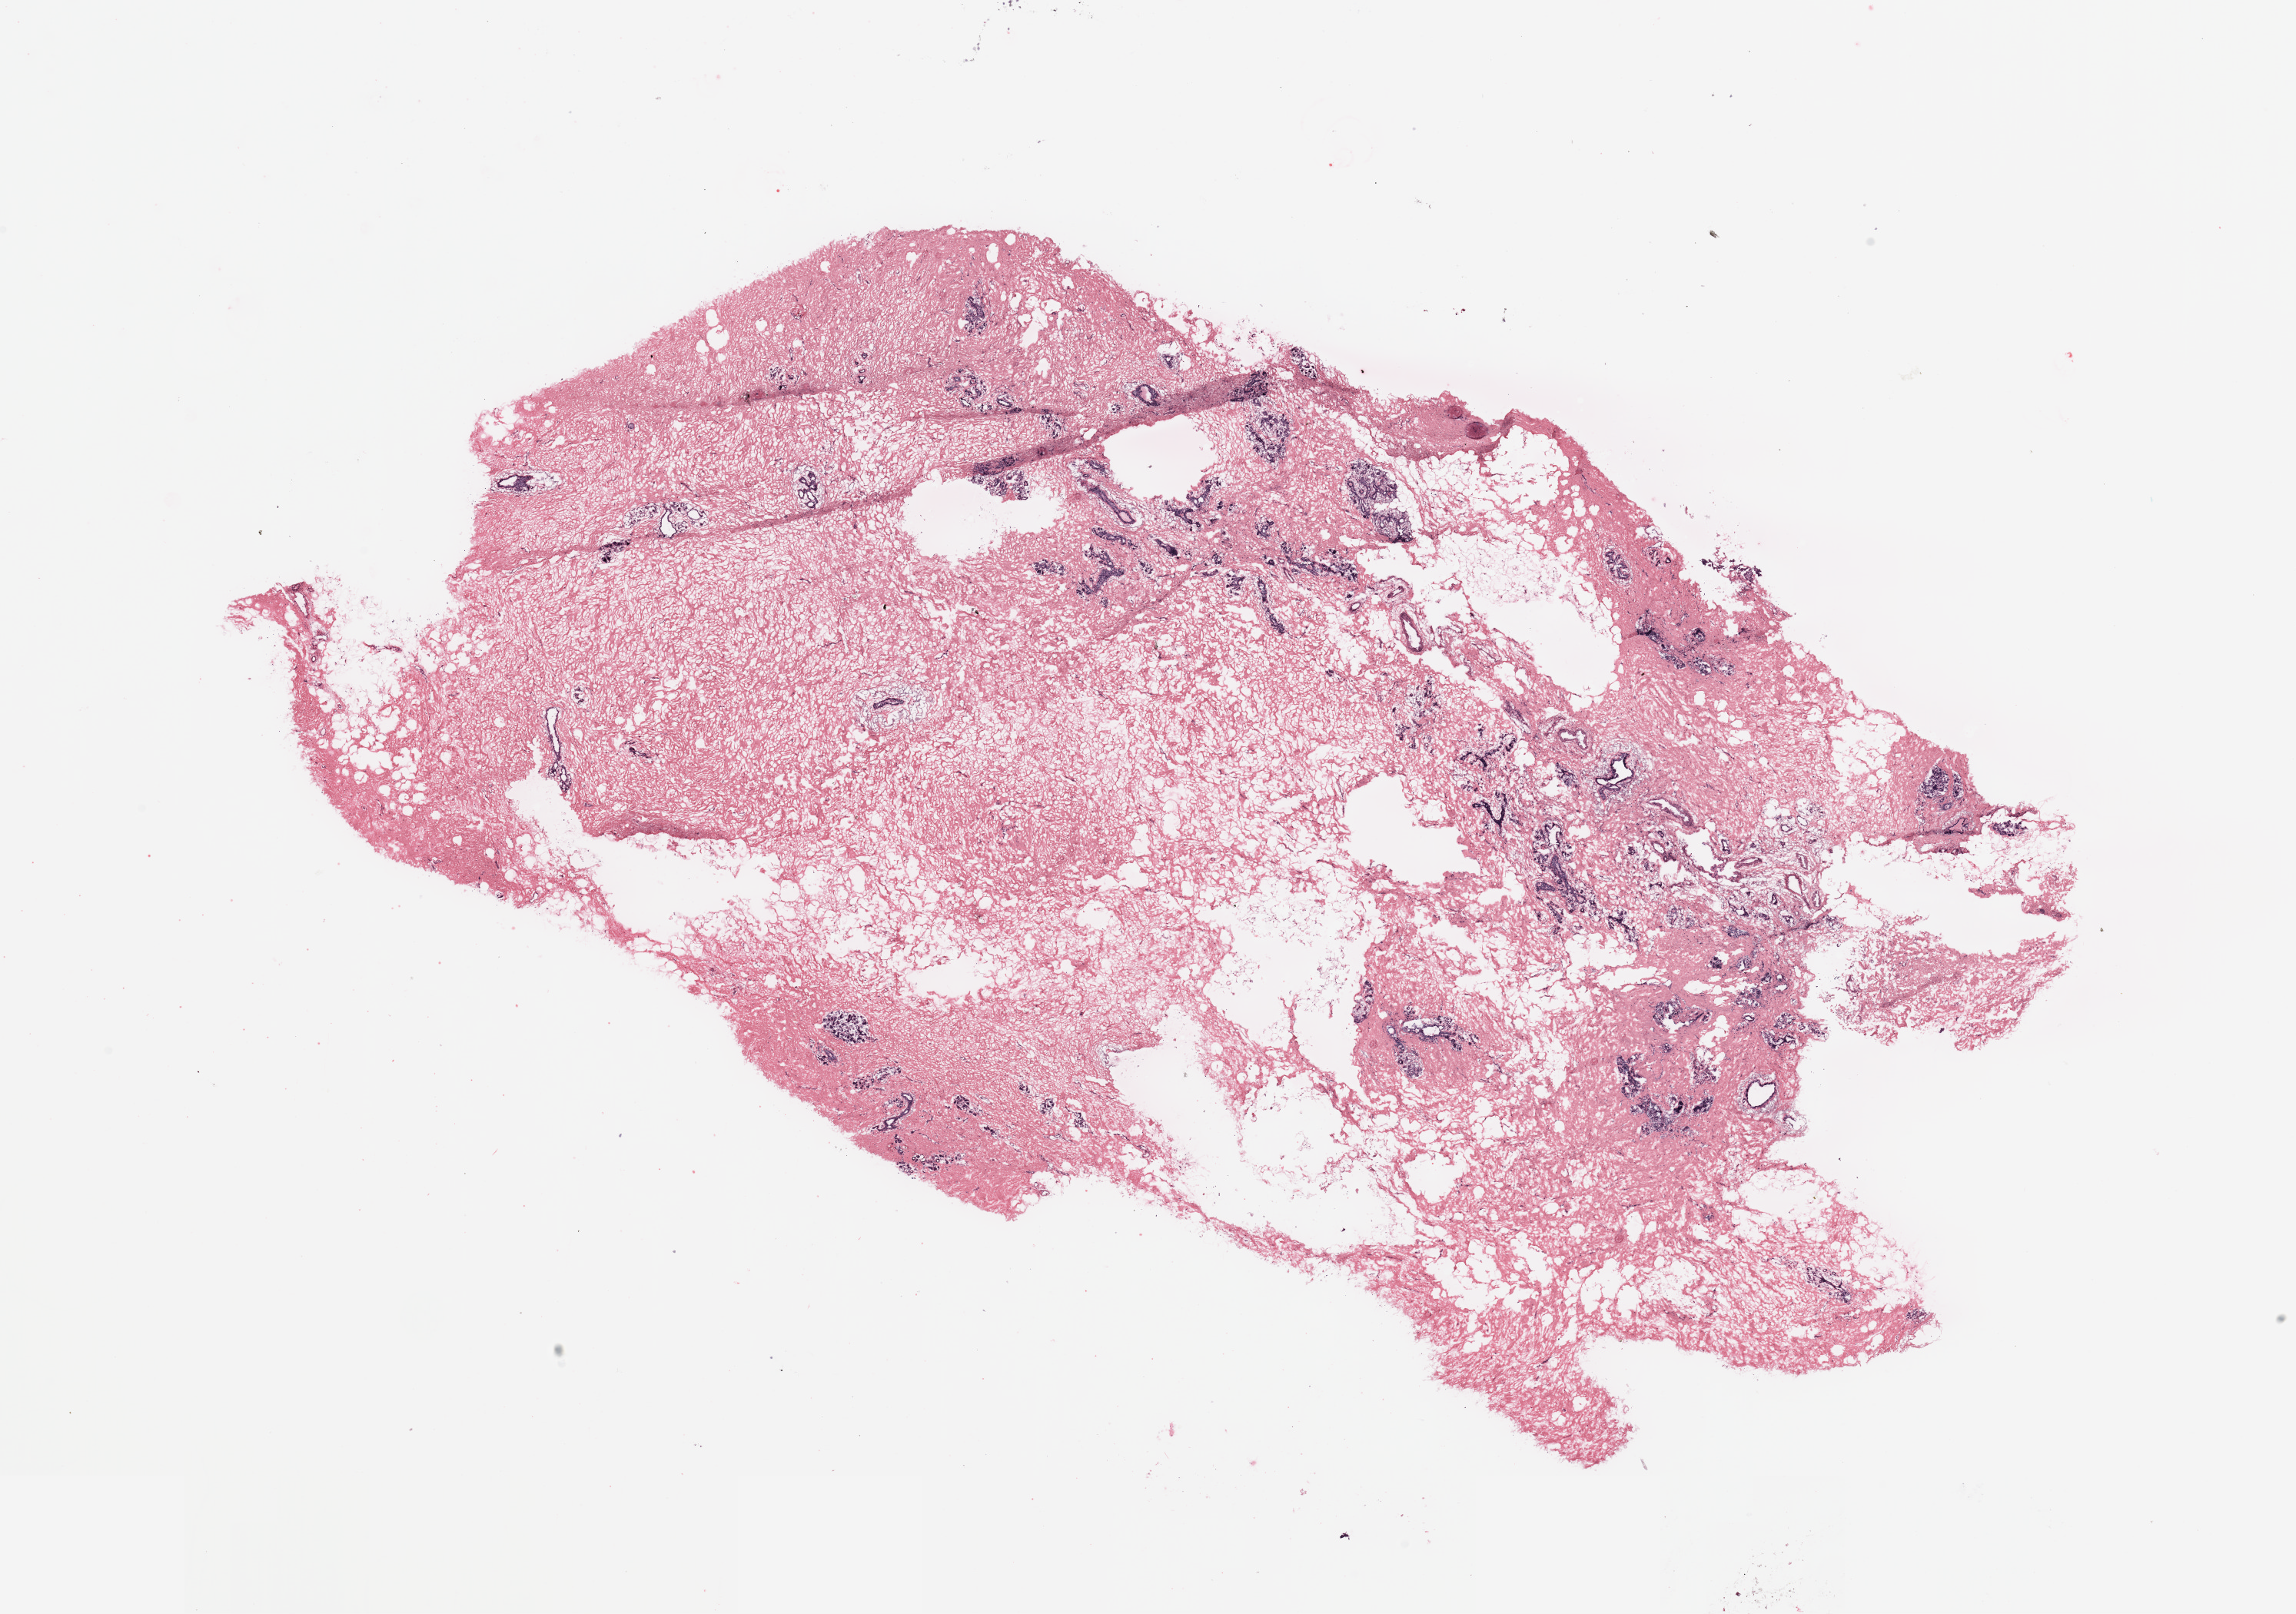
Digitized Hematoxylin and eosin (H&E) stained tissue section (whole slide), low-resolution overview of the scanned area, about 23.6 x 16.6 mm. Tumour tissue sample, breast. 59-year-old female patient.
Diagnosis: Infiltrating lobular carcinoma, NOS.